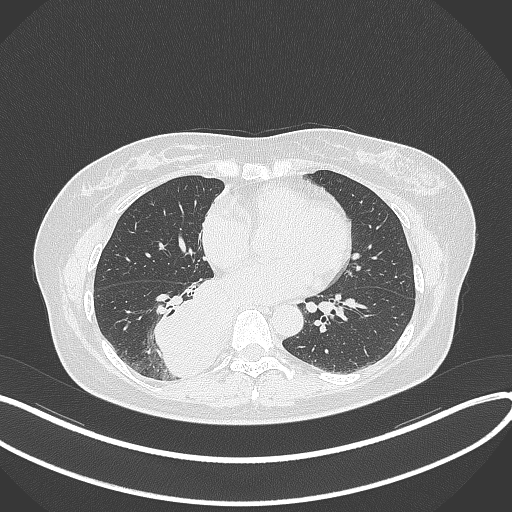
Chest CT, one axial slice; position 150 of 331 along the scan axis; reconstruction kernel B70f; lung window (W 1500 / L -600 HU); 1 mm slice thickness; 512 × 512 image matrix, field of view 400 × 400 mm. Female patient, age 54 years. Case-level facts recorded for this patient, not image findings: clinical TNM (as recorded): T4 N0 M0.
Structures marked on this image (bounding box drawn by a radiologist):
- lung tumour (recorded histology: adenocarcinoma): bounding box <156,277,225,379> (left, top, right, bottom; pixels)